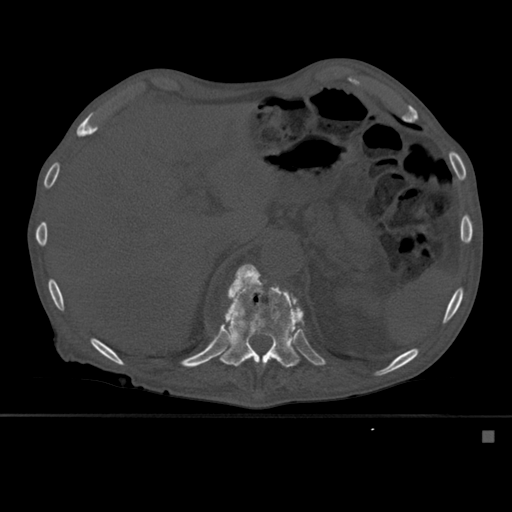
CT including the spine, one axial slice. Slice 280 of 527 in the series (ordered by position). Bone window (W 1800 / L 400 HU). 1.5 mm slice thickness. 512 × 512 image matrix. Male patient, age 78 years. Case-level facts recorded for this patient, not image findings: primary cancer: prostate.
Outlined on this slice (semi-automatic segmentation, software-assisted and operator-edited):
- T11 vertebra: bounding box <220,264,293,368> (left, top, right, bottom; pixels)
- T12 vertebra: <219,266,304,368>
- T9 vertebra: <224,350,230,360>